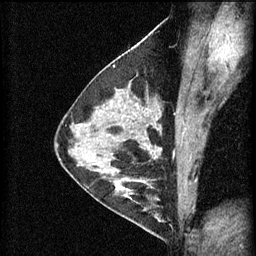
Breast MRI (dynamic contrast-enhanced), one sagittal slice. Slice 36 of 60 in the series (ordered by position). 3 images stored at this slice position (order not interpretable as contrast timing). 1.5 T. TE 4.2 ms, TR 11 ms. 2 mm slice thickness. 256 × 256 image matrix, field of view 180 × 180 mm. Patient: female, 29 years.
Outlined on this slice (semi-automatic segmentation, software-assisted and operator-edited):
- analysis volume of interest (the breast-tissue region the enhancement analysis was run in; not a lesion): box from (x=105, y=172) to (x=171, y=227) px
- tumour enhancement mask (voxels above the 70 % enhancement threshold inside the analysis volume of interest): (x=105, y=172)–(x=162, y=223)